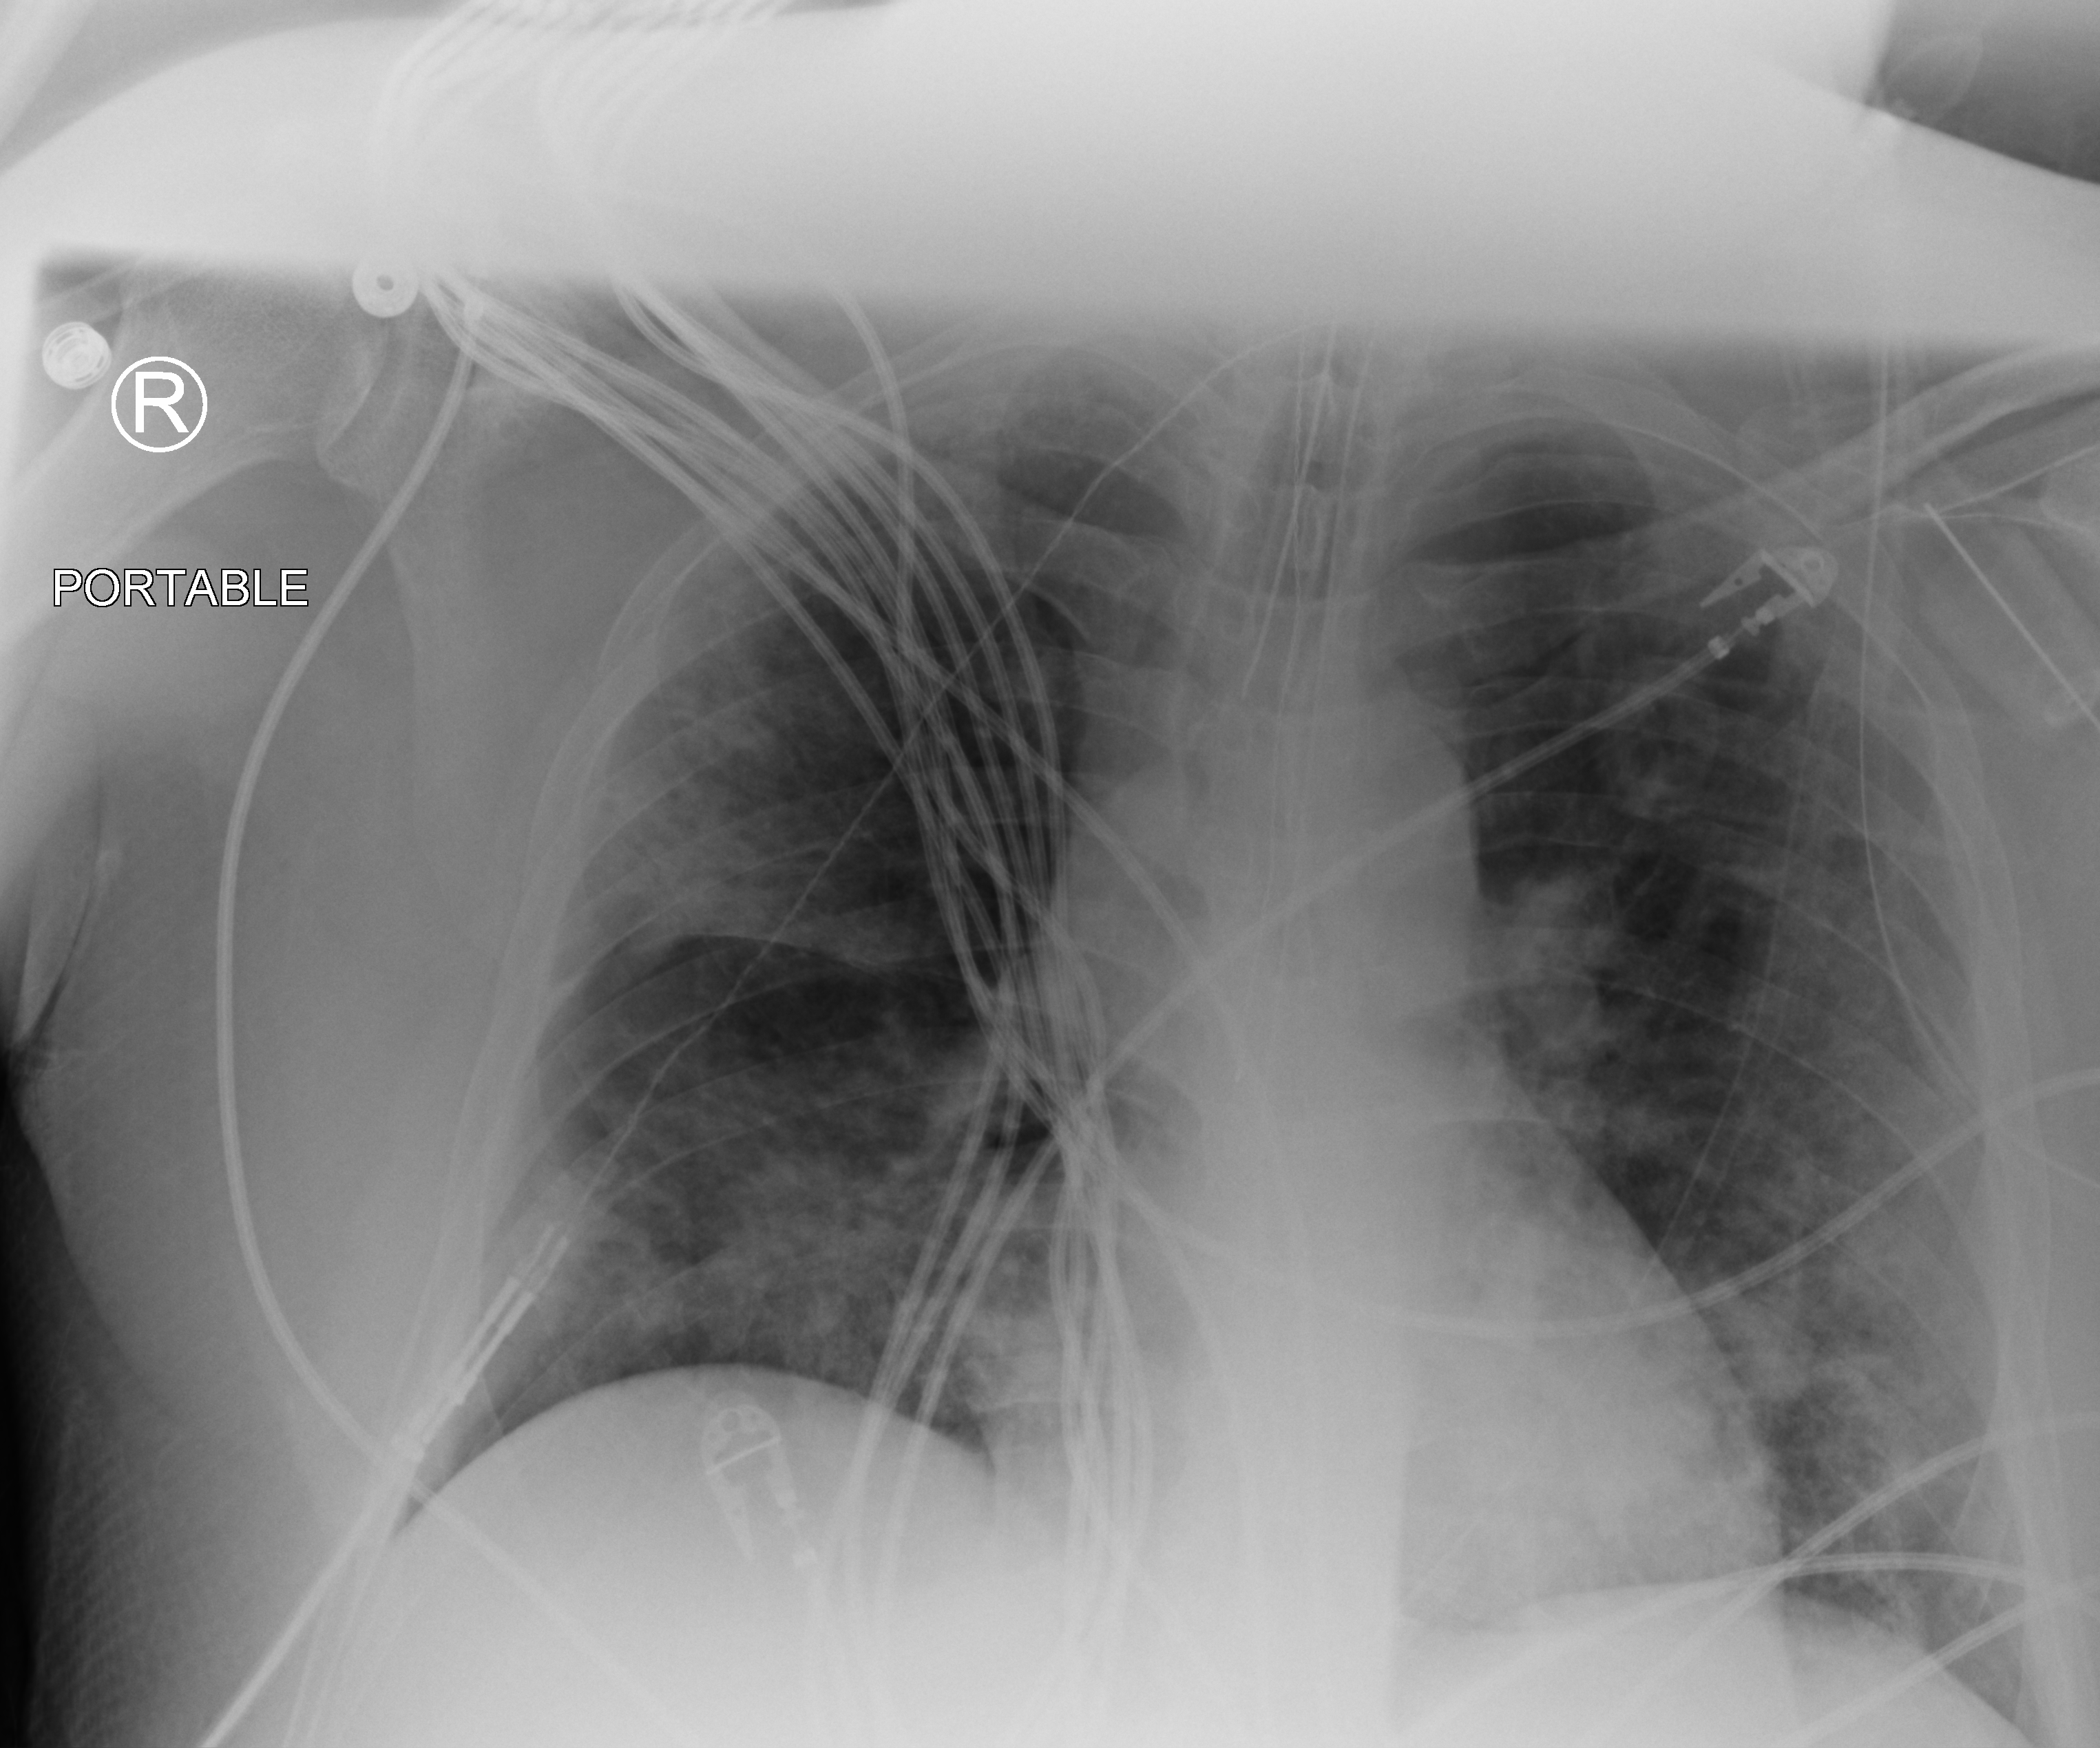
Chest X-ray (portable); anteroposterior (AP) projection. Adult patient hospitalised with COVID-19, age 18–59 years.
Hospital-stay facts (about this admission, not read from this image; timing relative to this image not recorded): mechanically ventilated during this hospital stay: yes.